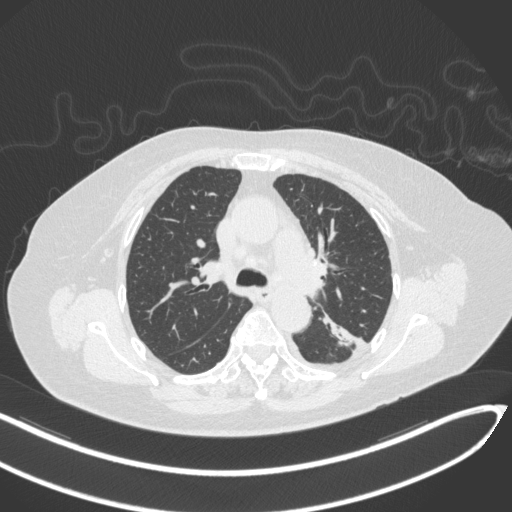
Chest CT, one axial slice; slice 209 of 270 in the series (ordered by position); reconstruction kernel B31f; lung window (W 1500 / L -600 HU); 1 mm slice thickness; 512 × 512 image matrix. Female patient, age 76 years. Case-level facts recorded for this patient, not image findings: clinical TNM (as recorded): T1c N0 M0.
Structures marked on this image (bounding box drawn by a radiologist):
- lung tumour (recorded histology: adenocarcinoma): bounding box (x1, y1, x2, y2) in pixels: (326, 314, 361, 350)